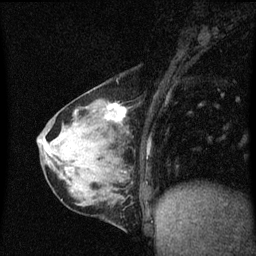
Breast MRI (dynamic contrast-enhanced), one sagittal slice. Position 19 of 60 along the scan axis. Dynamic contrast-enhanced series, image 2 of 3 at this slice position (ordered by acquisition). 1.5 T. TE 4.2 ms, TR 8.4 ms. 2 mm slice thickness. 256 × 256 image matrix. Female patient, age 64 years. Case-level facts recorded for this patient, not image findings: setting: breast cancer imaged before/during neoadjuvant chemotherapy; receptor status: HR-positive, HER2-negative.
Outlined on this slice (semi-automatically segmented with operator editing):
- analysis volume of interest (the breast-tissue region the enhancement analysis was run in; not a lesion): bounding box [x1, y1, x2, y2] px = [65, 96, 130, 157]
- tumour enhancement mask (voxels above the 70 % enhancement threshold inside the analysis volume of interest): [110, 104, 126, 119]